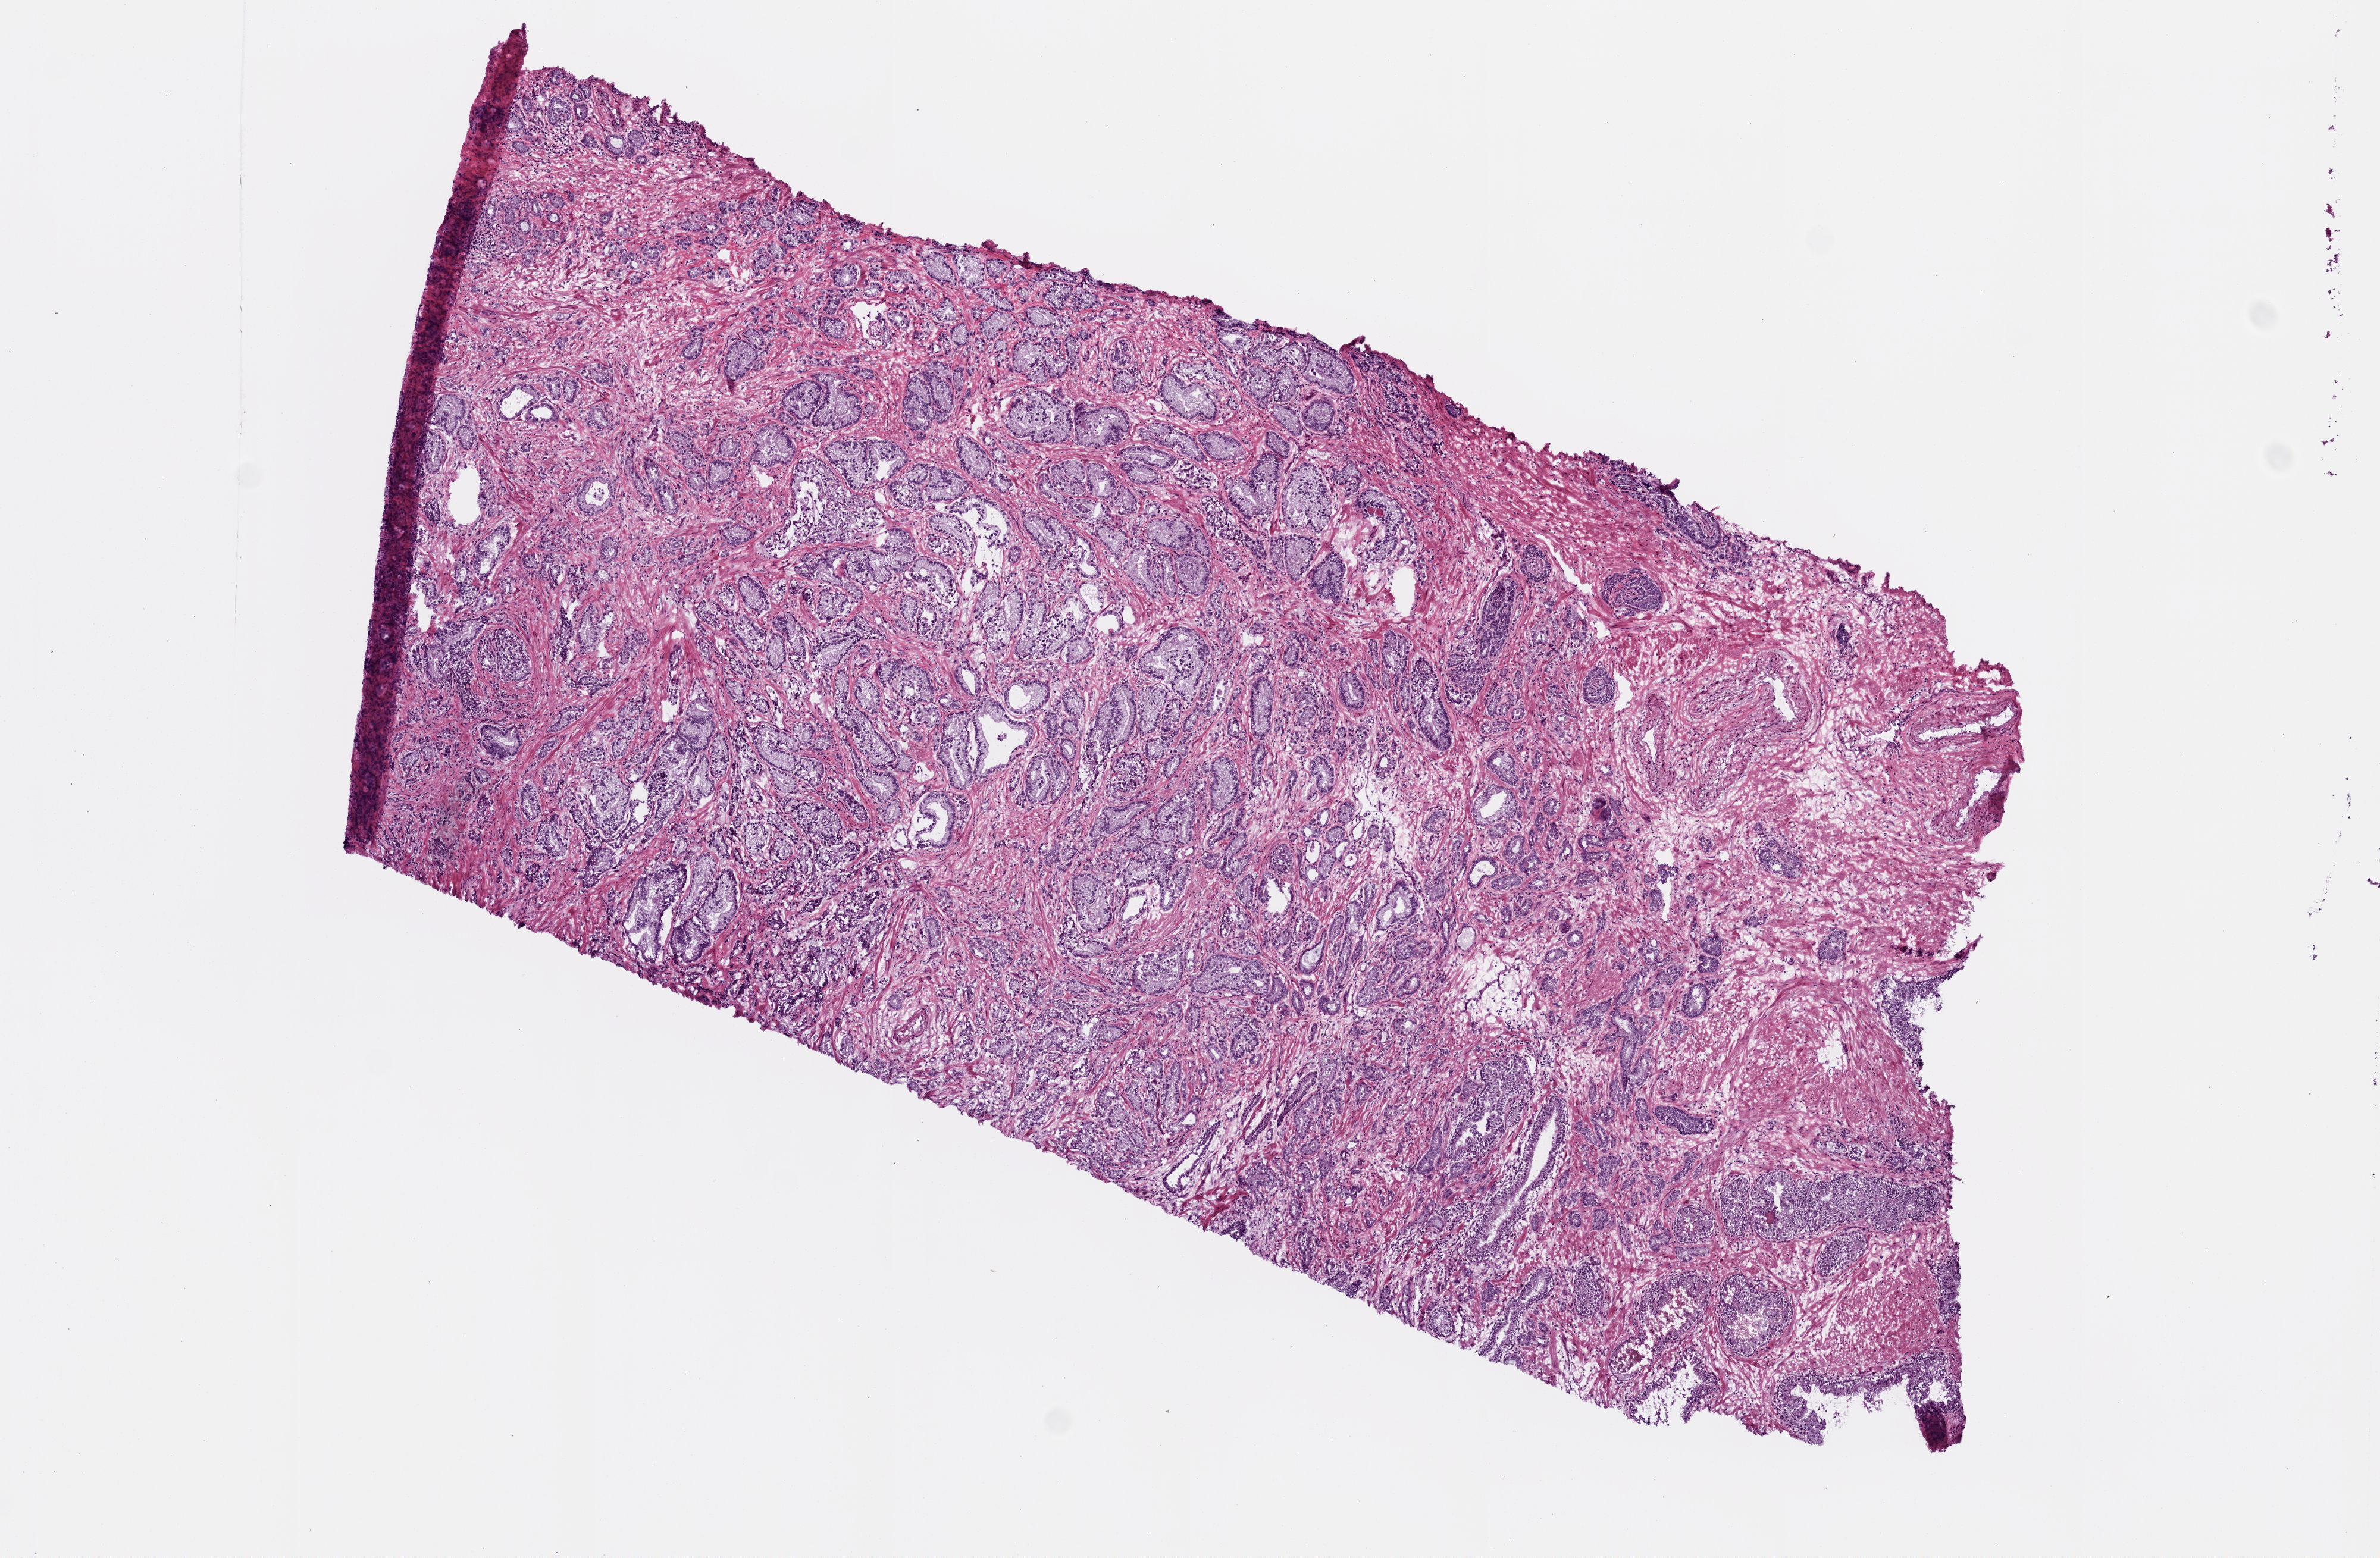
Digitized H&E tissue section (whole slide), shown as a low-resolution overview of the whole scanned area (about 8.0 x 5.3 mm), frozen section from the top of the tissue portion, sample: primary tumour, prostate. Male patient; age at initial diagnosis 65 years. Gleason score: 7 (3+4). Slide review estimates, as recorded: tumour cells 60%, tumour nuclei 70%, normal cells 20%, stromal cells 20%, necrosis 0%. Inflammatory infiltration, as recorded: lymphocyte infiltration 0%, monocyte infiltration 0%, neutrophil infiltration 0%.
Pathologic diagnosis: Acinar cell carcinoma (prostate gland).